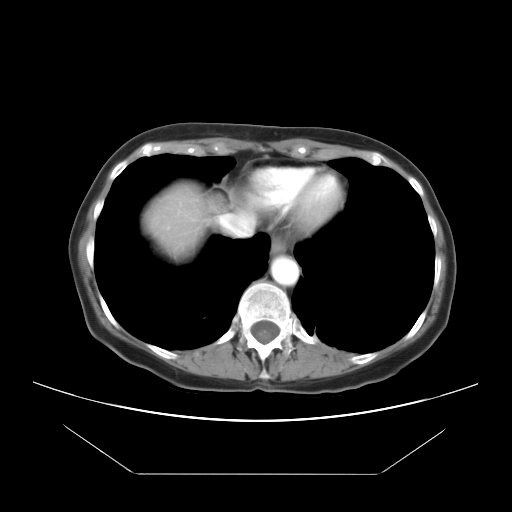
Contrast-enhanced abdominal CT, one axial slice; position 20 of 21 along the scan axis; reconstruction kernel STANDARD; 120 kVp; intravenous contrast given; soft-tissue window (W 400 / L 40 HU); 512 × 512 image matrix. Female patient, age 72 years. From the clinical record (not read from this slice): diagnosis: colorectal cancer liver metastases, imaged before liver resection; multiple liver metastases: yes.
Outlined on this slice (manually delineated by an expert):
- liver: bounding box (x1, y1, x2, y2) in pixels: (147, 184, 208, 255)
- planned liver remnant (the part of the liver to remain after resection): (147, 185, 208, 237)